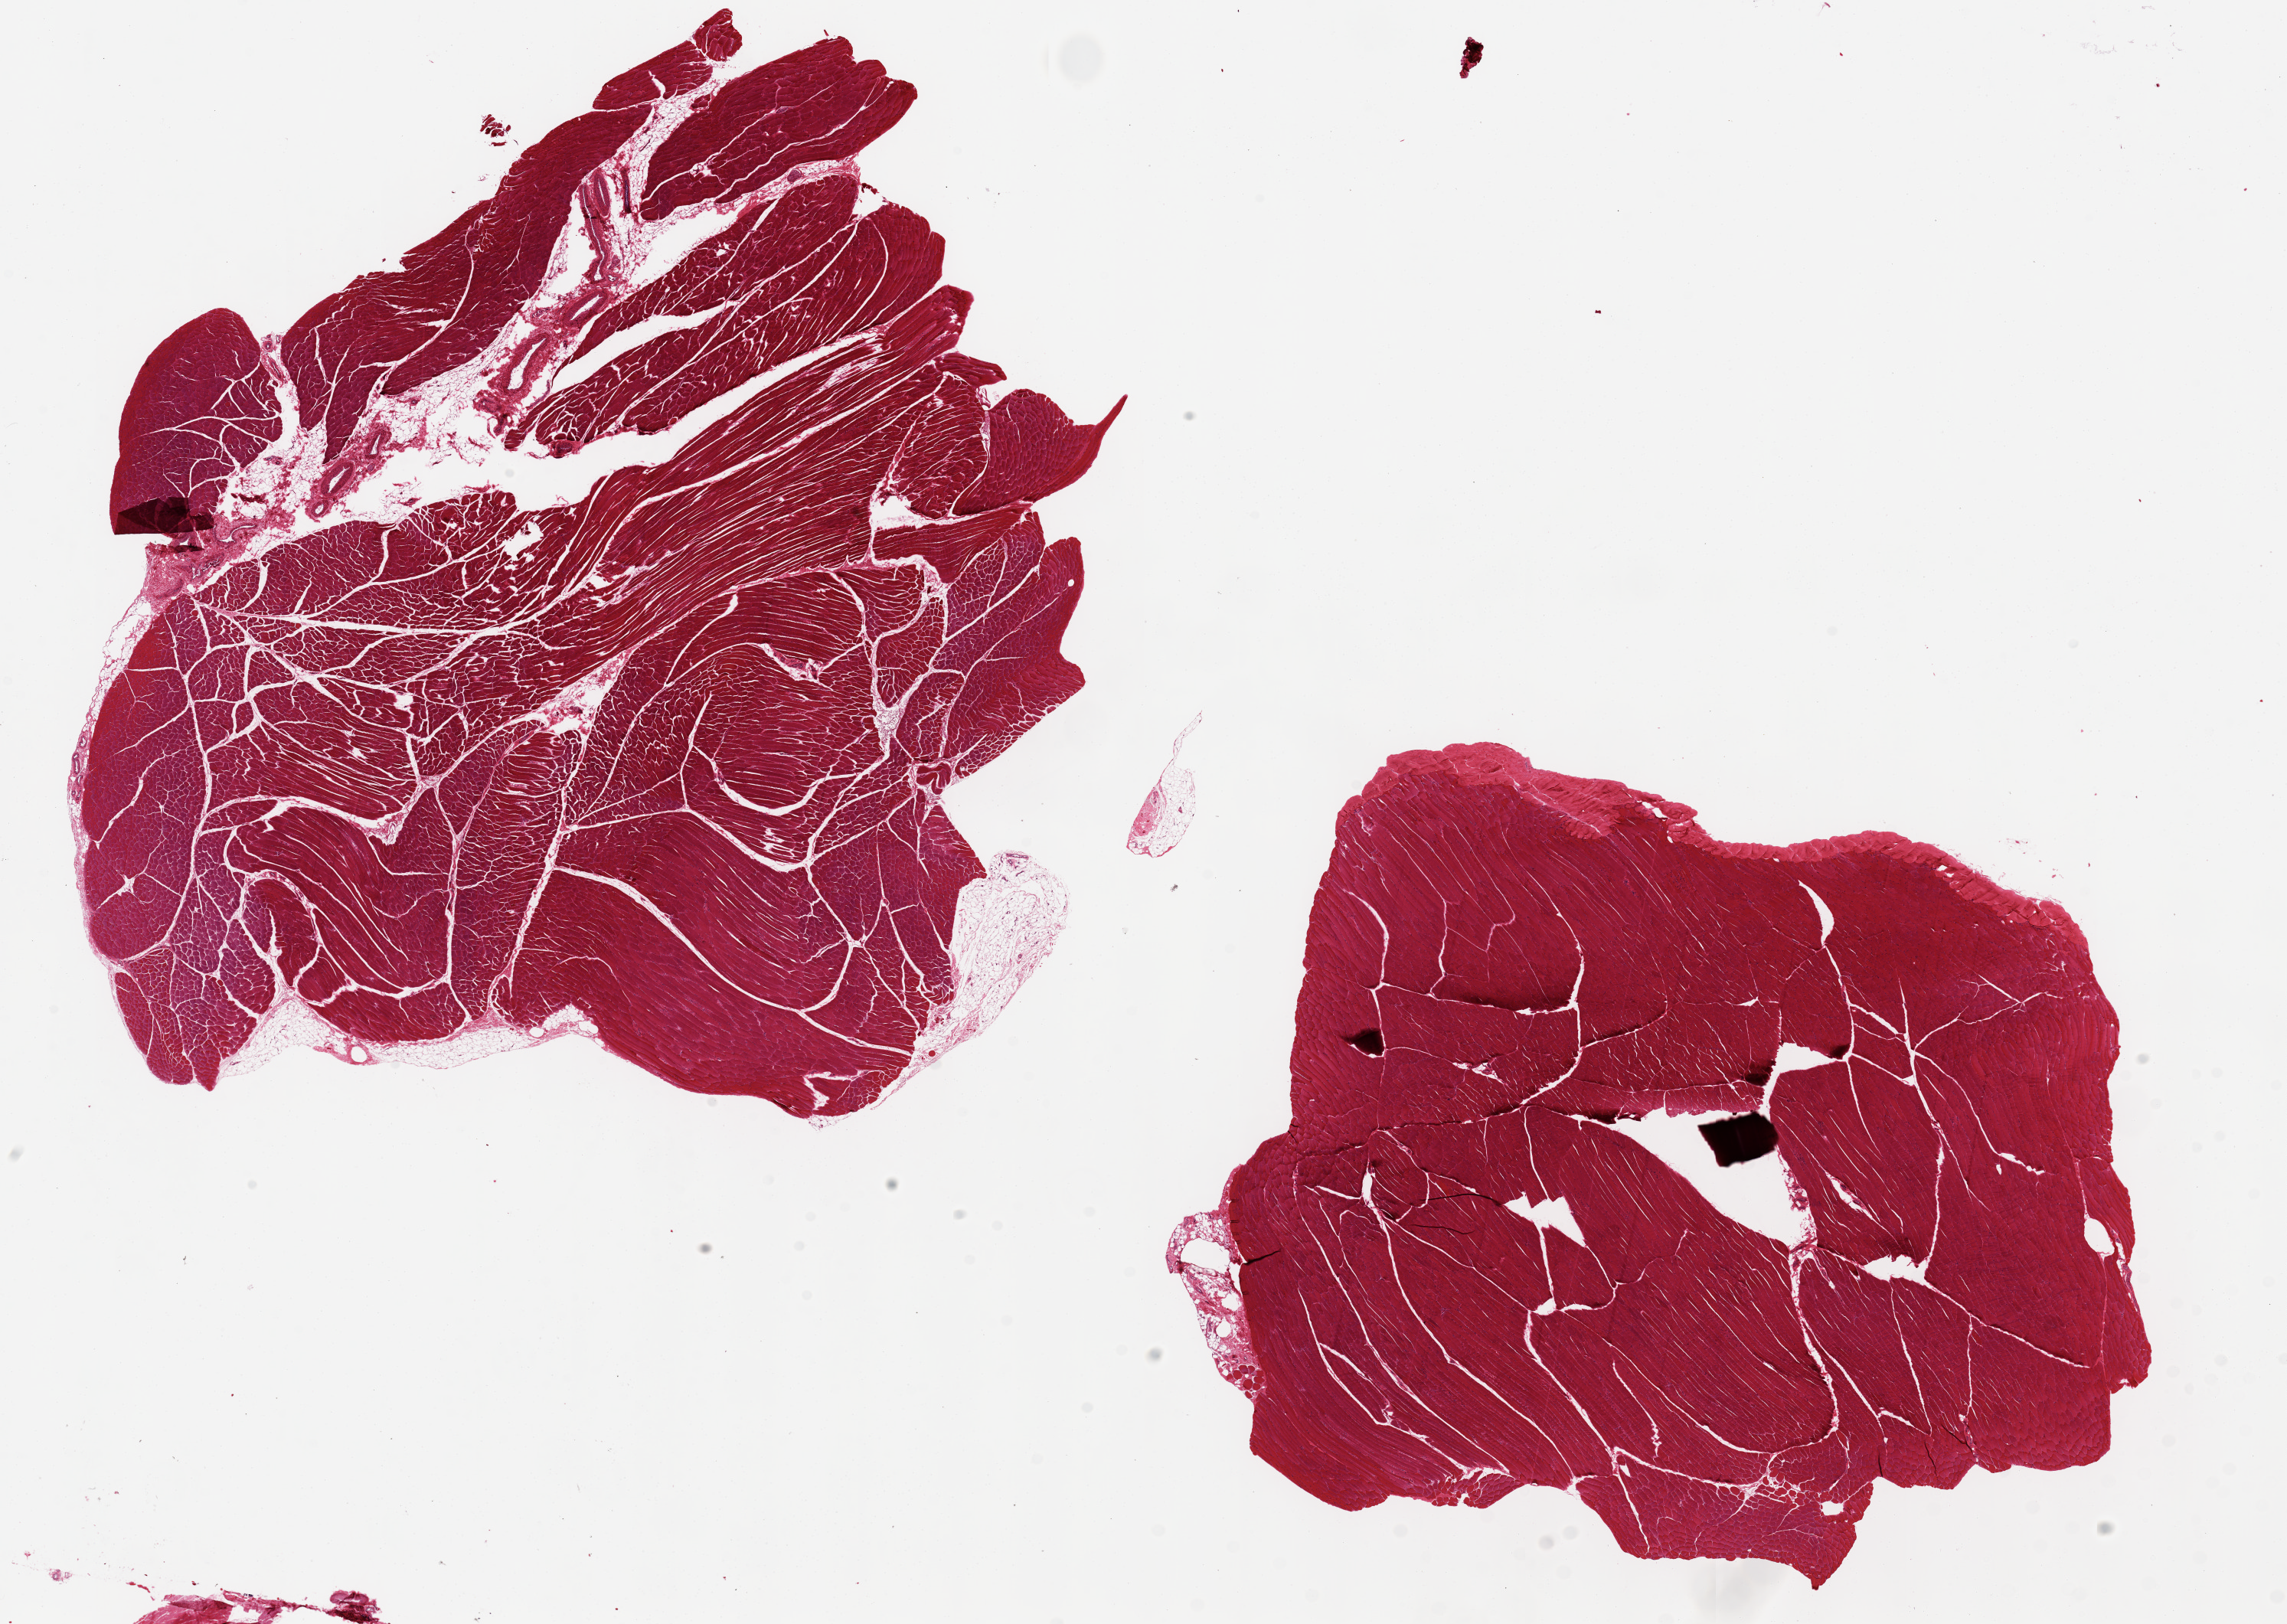
Hematoxylin and eosin (H&E) whole-slide image, a low-resolution overview of the entire scanned area, about 23.6 x 16.8 mm (from a 20x scan). PAXgene-fixed paraffin-embedded (PFPE) section. Sampled site (target tissue): skeletal muscle. Donor tissue sample. Donor: female.
* review note (as recorded): 2 pieces, ~10x10 mm; one with 10% fat